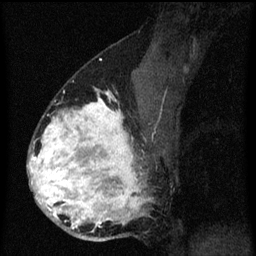
Breast MRI (dynamic contrast-enhanced), one sagittal slice. Position 38 of 60 along the scan axis. Dynamic contrast-enhanced series, image 2 of 3 at this slice position (ordered by acquisition). 1.5 T. TE 4.2 ms, TR 8.4 ms. 256 × 256 image matrix, field of view 180 × 180 mm. Patient: female, 34 years. Case-level facts recorded for this patient, not image findings: setting: breast cancer imaged before/during neoadjuvant chemotherapy; receptor status: HR-positive, HER2-negative.
Structures marked on this image (semi-automatic segmentation, software-assisted and operator-edited):
- analysis volume of interest (the breast-tissue region the enhancement analysis was run in; not a lesion): bounding box <28,60,157,243> (left, top, right, bottom; pixels)
- tumour enhancement mask (voxels above the 70 % enhancement threshold inside the analysis volume of interest): <28,92,151,229>